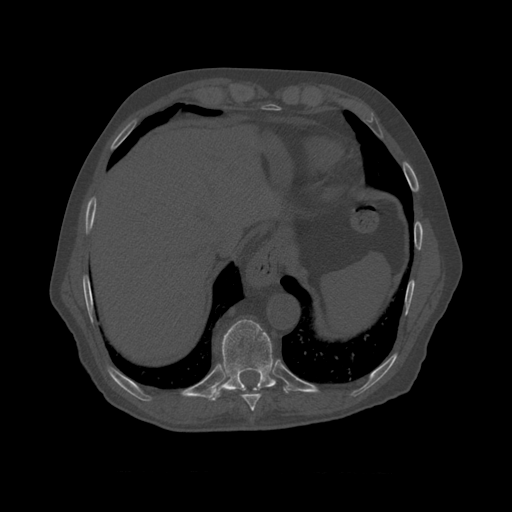
CT including the spine, one axial slice. Slice 433 of 450 in the series (ordered by position). Reconstruction kernel STANDARD. Bone window (W 1800 / L 400 HU). 512 × 512 image matrix, field of view 405 × 405 mm. Patient age 75 years. From the clinical record (not read from this slice): primary cancer: prostate.
Annotated regions visible in this slice (semi-automatically segmented with operator editing):
- T8 vertebra: bounding box (x1, y1, x2, y2) in pixels: (241, 388, 262, 410)
- T9 vertebra: (216, 319, 285, 396)